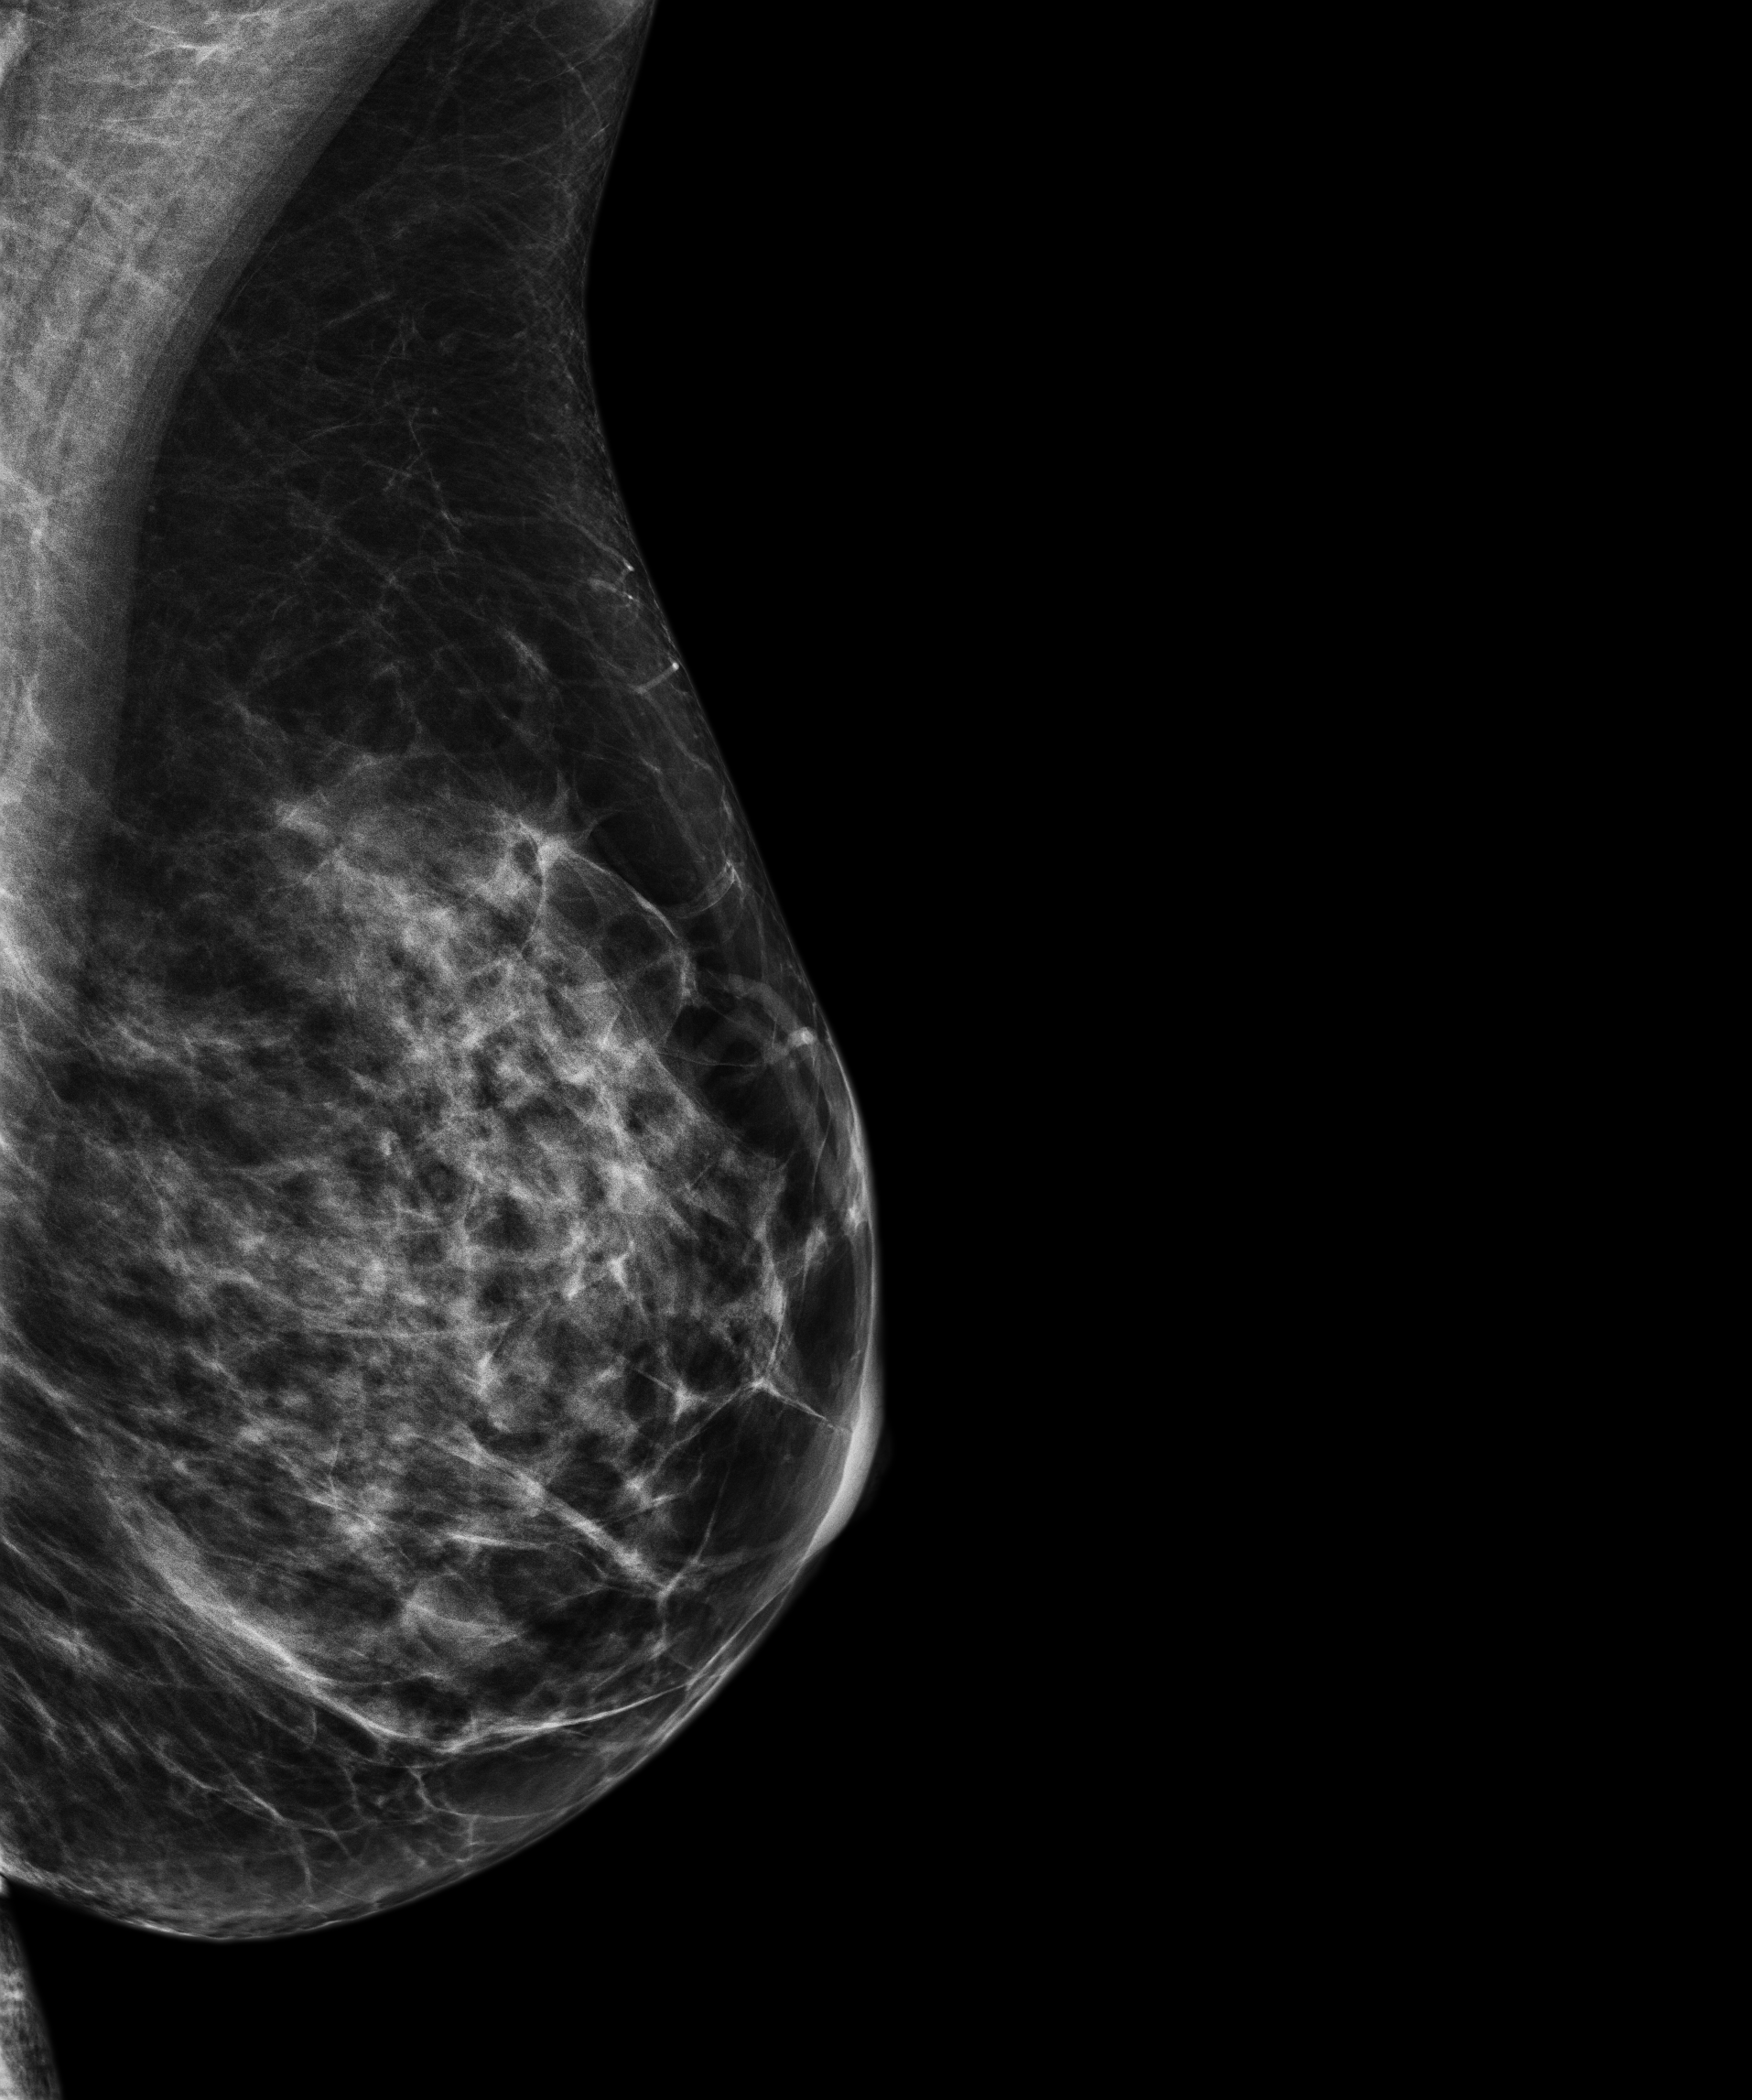
Annual screening mammography examination; system: Senographe Pristina. Female patient, age 46 years.
Image type: full-field digital mammogram. Breast: left. Projection: MLO view.